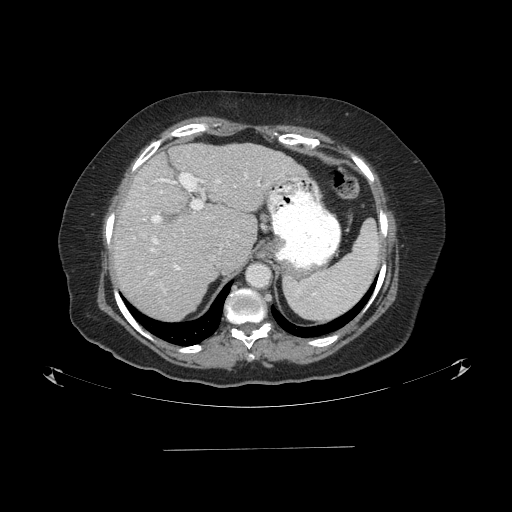
Contrast-enhanced abdominal CT (liver protocol), one axial slice. Slice 64 of 103 in the series (ordered by position). Reconstruction kernel STANDARD. 120 kVp. One of 2 acquisitions stored at this slice position. Soft-tissue window (W 400 / L 40 HU). 512 × 512 image matrix. Case-level facts recorded for this patient, not image findings: diagnosis: hepatocellular carcinoma (patient treated with transarterial chemoembolisation; whether this scan precedes or follows treatment is not stated here); TNM stage (as recorded): Stage-IIIA; Child-Pugh class: A; tumour differentiation: poorly differentiated; tumour nodularity: multinodular.
Outlined on this slice (semi-automatic segmentation, software-assisted and operator-edited):
- abdominal aorta: bounding box [x1, y1, x2, y2] px = [248, 264, 271, 287]
- liver parenchyma outside the tumour (the mass and vessels are separate outlines, so this box may not span the whole liver): [112, 143, 304, 320]
- liver vessels: [143, 173, 297, 275]